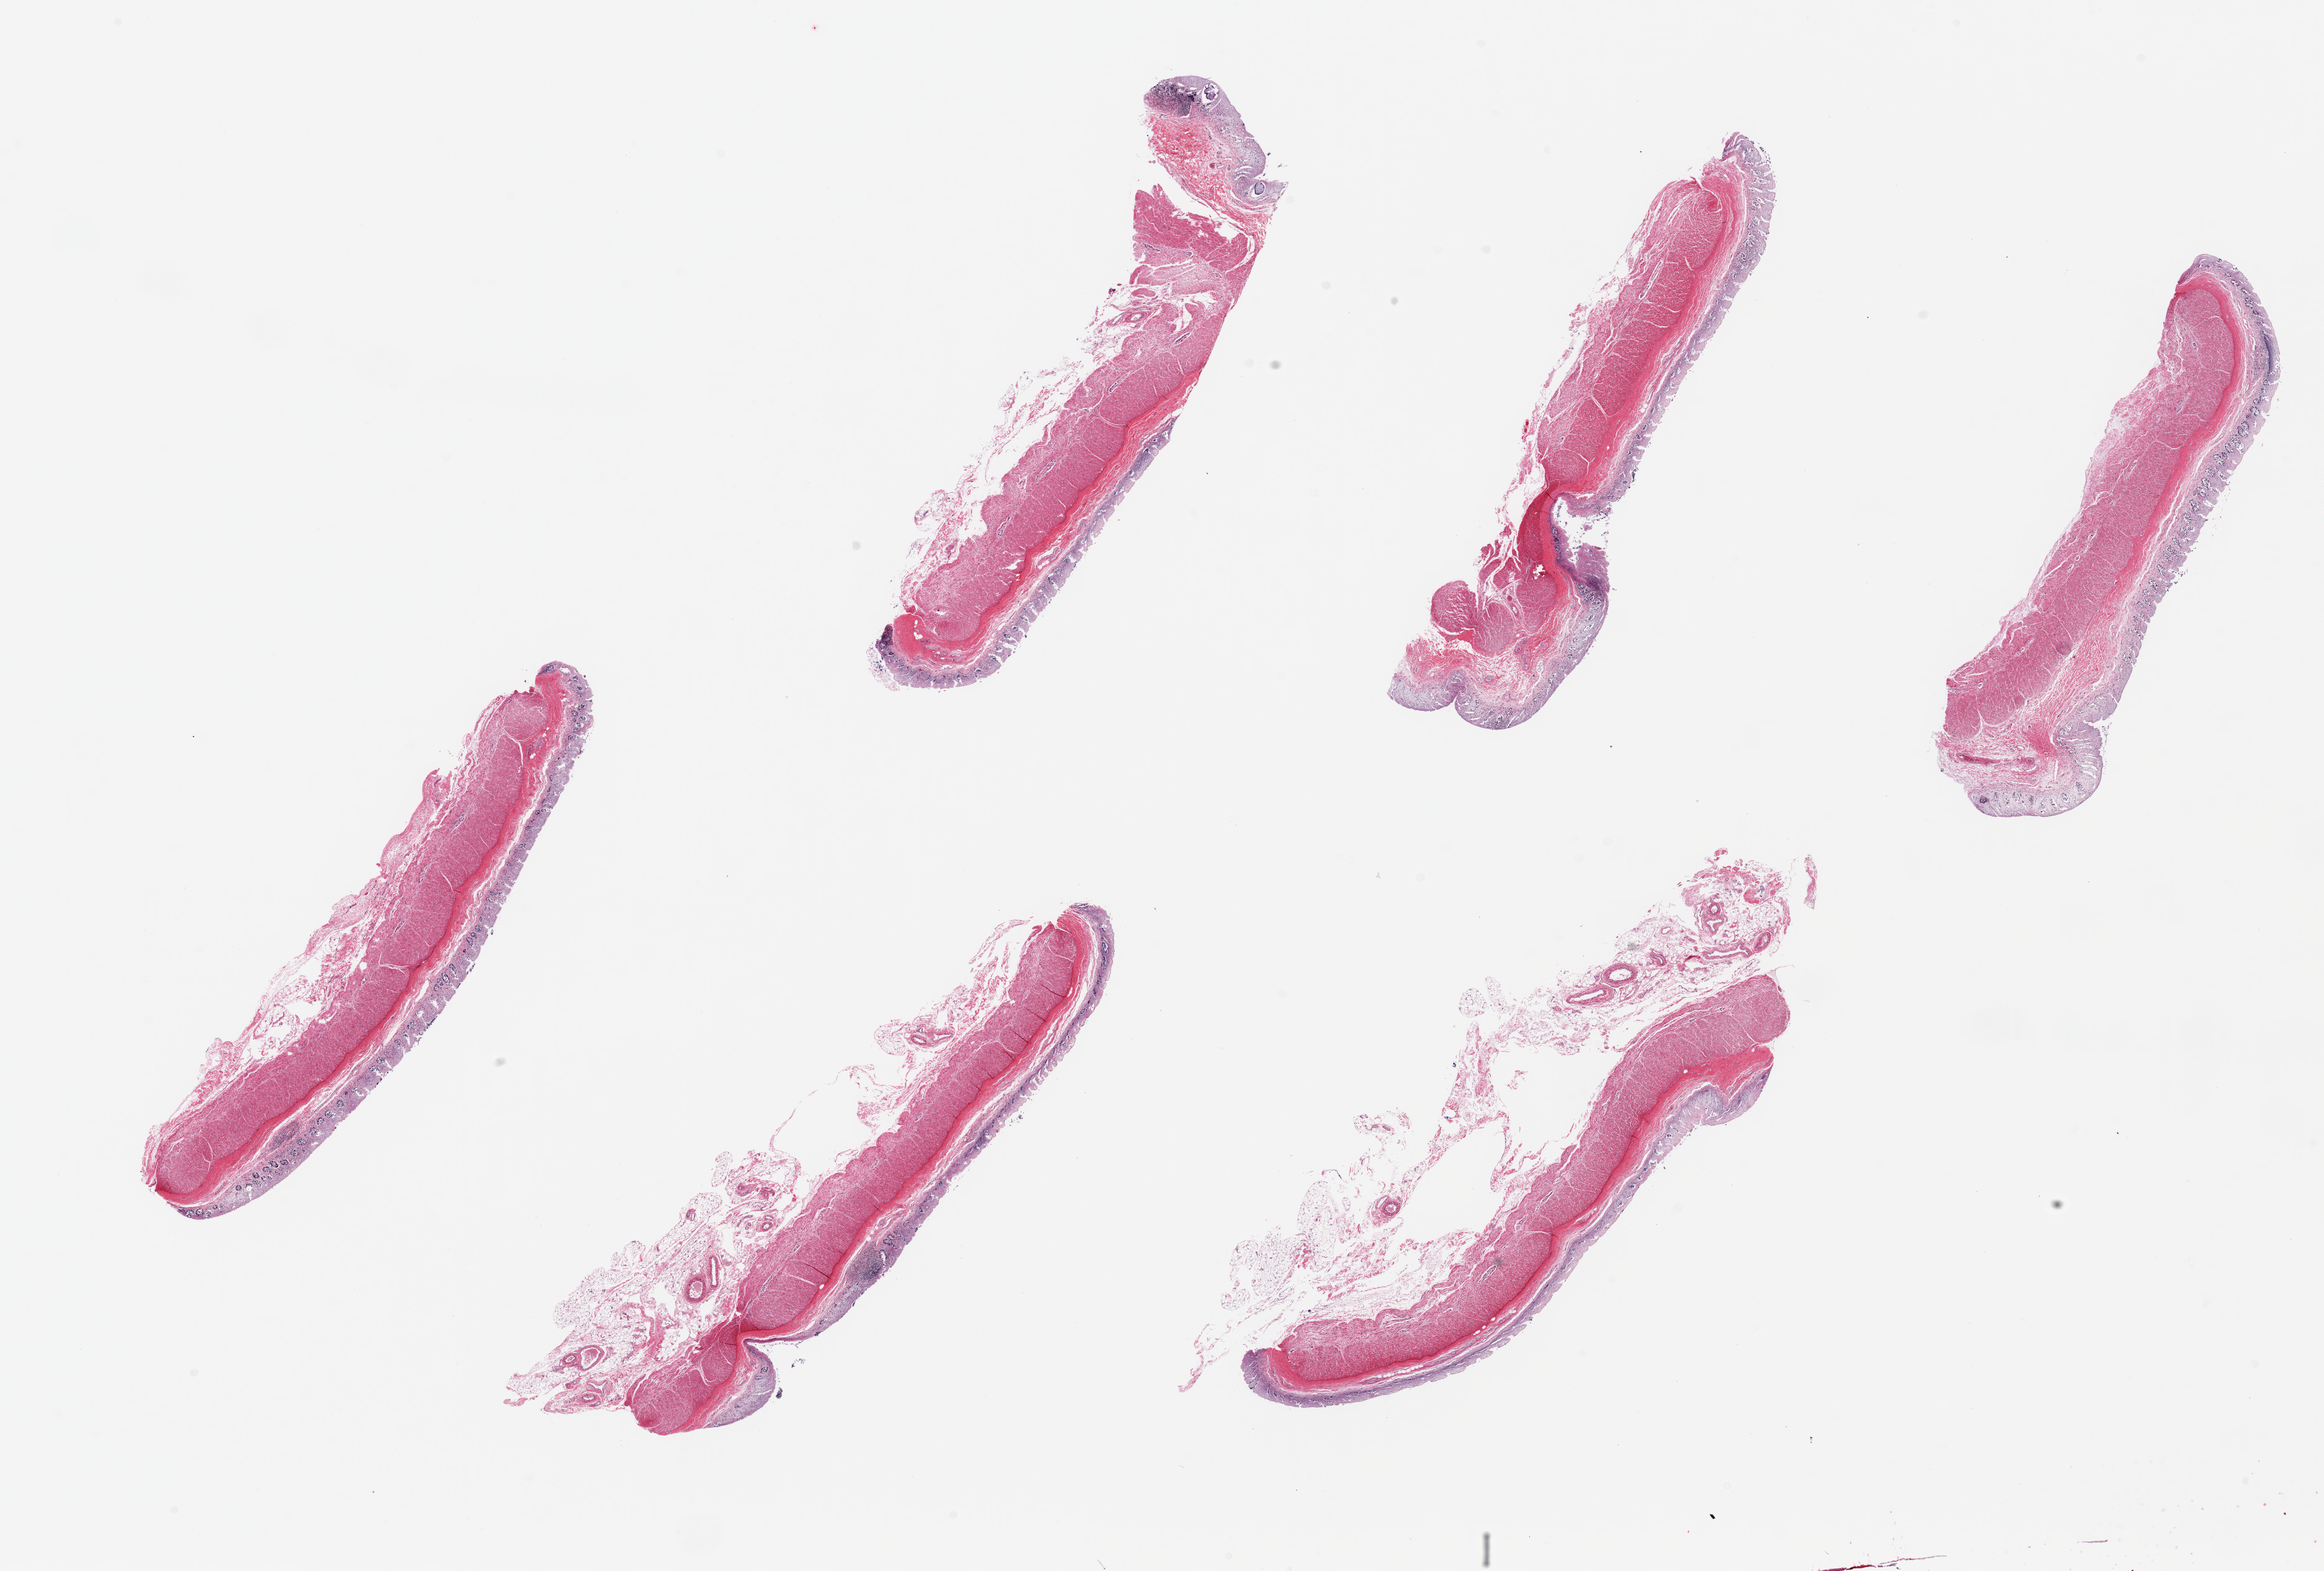
Haematoxylin and eosin whole-slide image, brightfield, shown as a low-resolution overview of the whole scanned area (about 29.5 x 20.0 mm); PAXgene-fixed, paraffin-embedded tissue; sampled site (target tissue): sigmoid colon; tissue donor sample. Donor: male.
Review note (as recorded): 6 pieces ~8x1.5mm. 80% muscularis propria. Badly autolyzed.